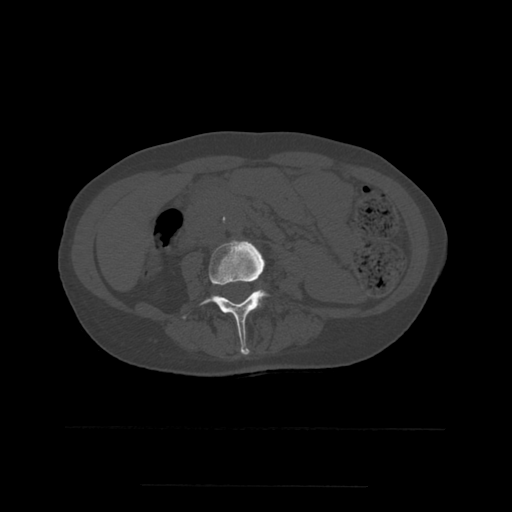
CT including the spine, one axial slice; position 186 of 544 along the scan axis; bone window (W 1800 / L 400 HU); 1.25 mm slice thickness; 512 × 512 image matrix, field of view 350 × 350 mm. Patient age 58 years. Case-level facts recorded for this patient, not image findings: primary cancer: lung.
Outlined on this slice (semi-automatic segmentation, software-assisted and operator-edited):
- L3 vertebra: bounding box [x1, y1, x2, y2] px = [183, 240, 270, 355]
- L4 vertebra: [258, 290, 267, 301]